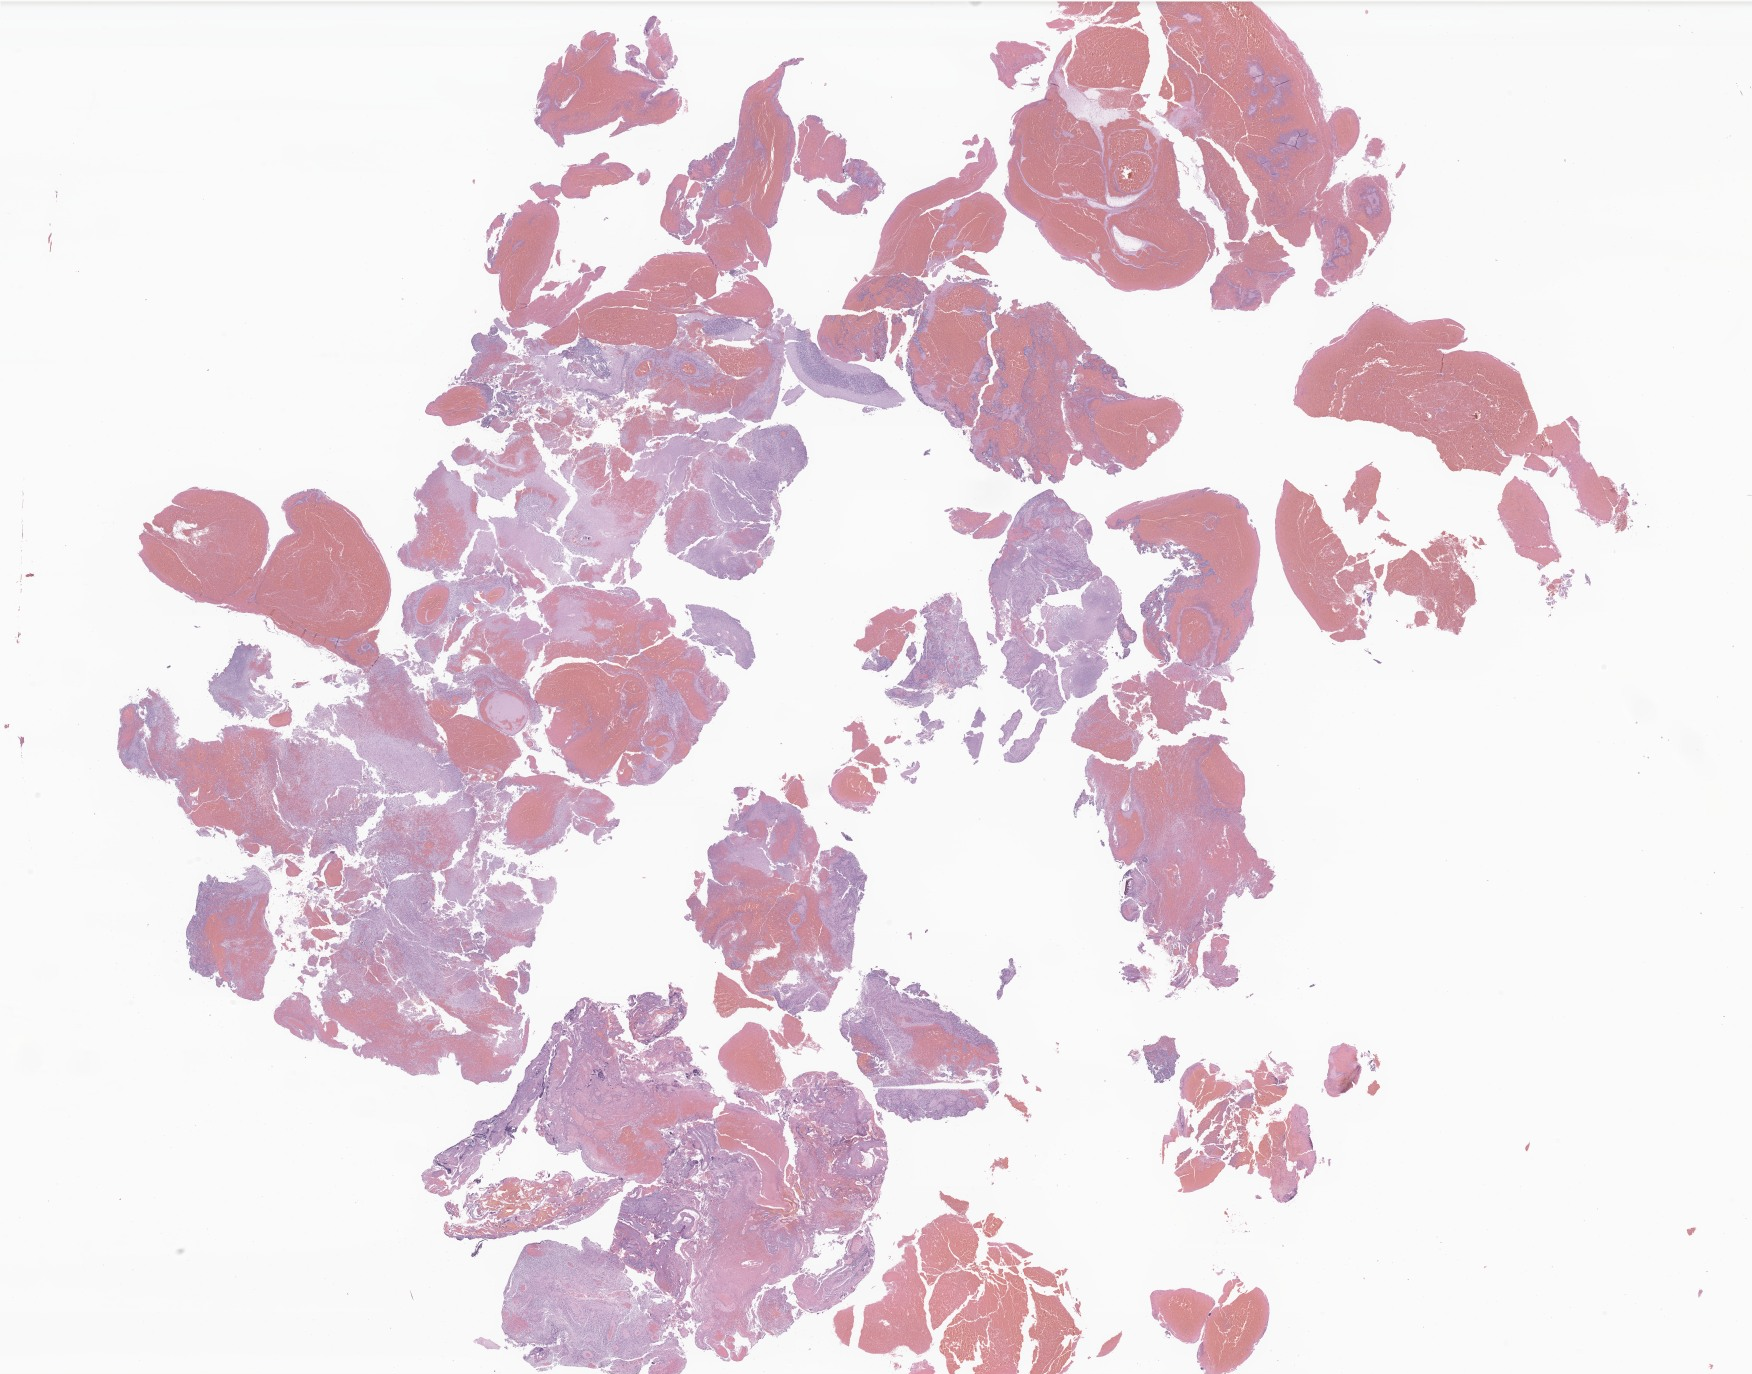
Hematoxylin and eosin (H&E) whole-slide image of tumor tissue from the brain, low-resolution overview of the scanned area, about 29.6 x 23.2 mm, FFPE section. Patient male; age 574 days (about 1.6 years).
Recorded diagnosis: Ependymoma, NOS.